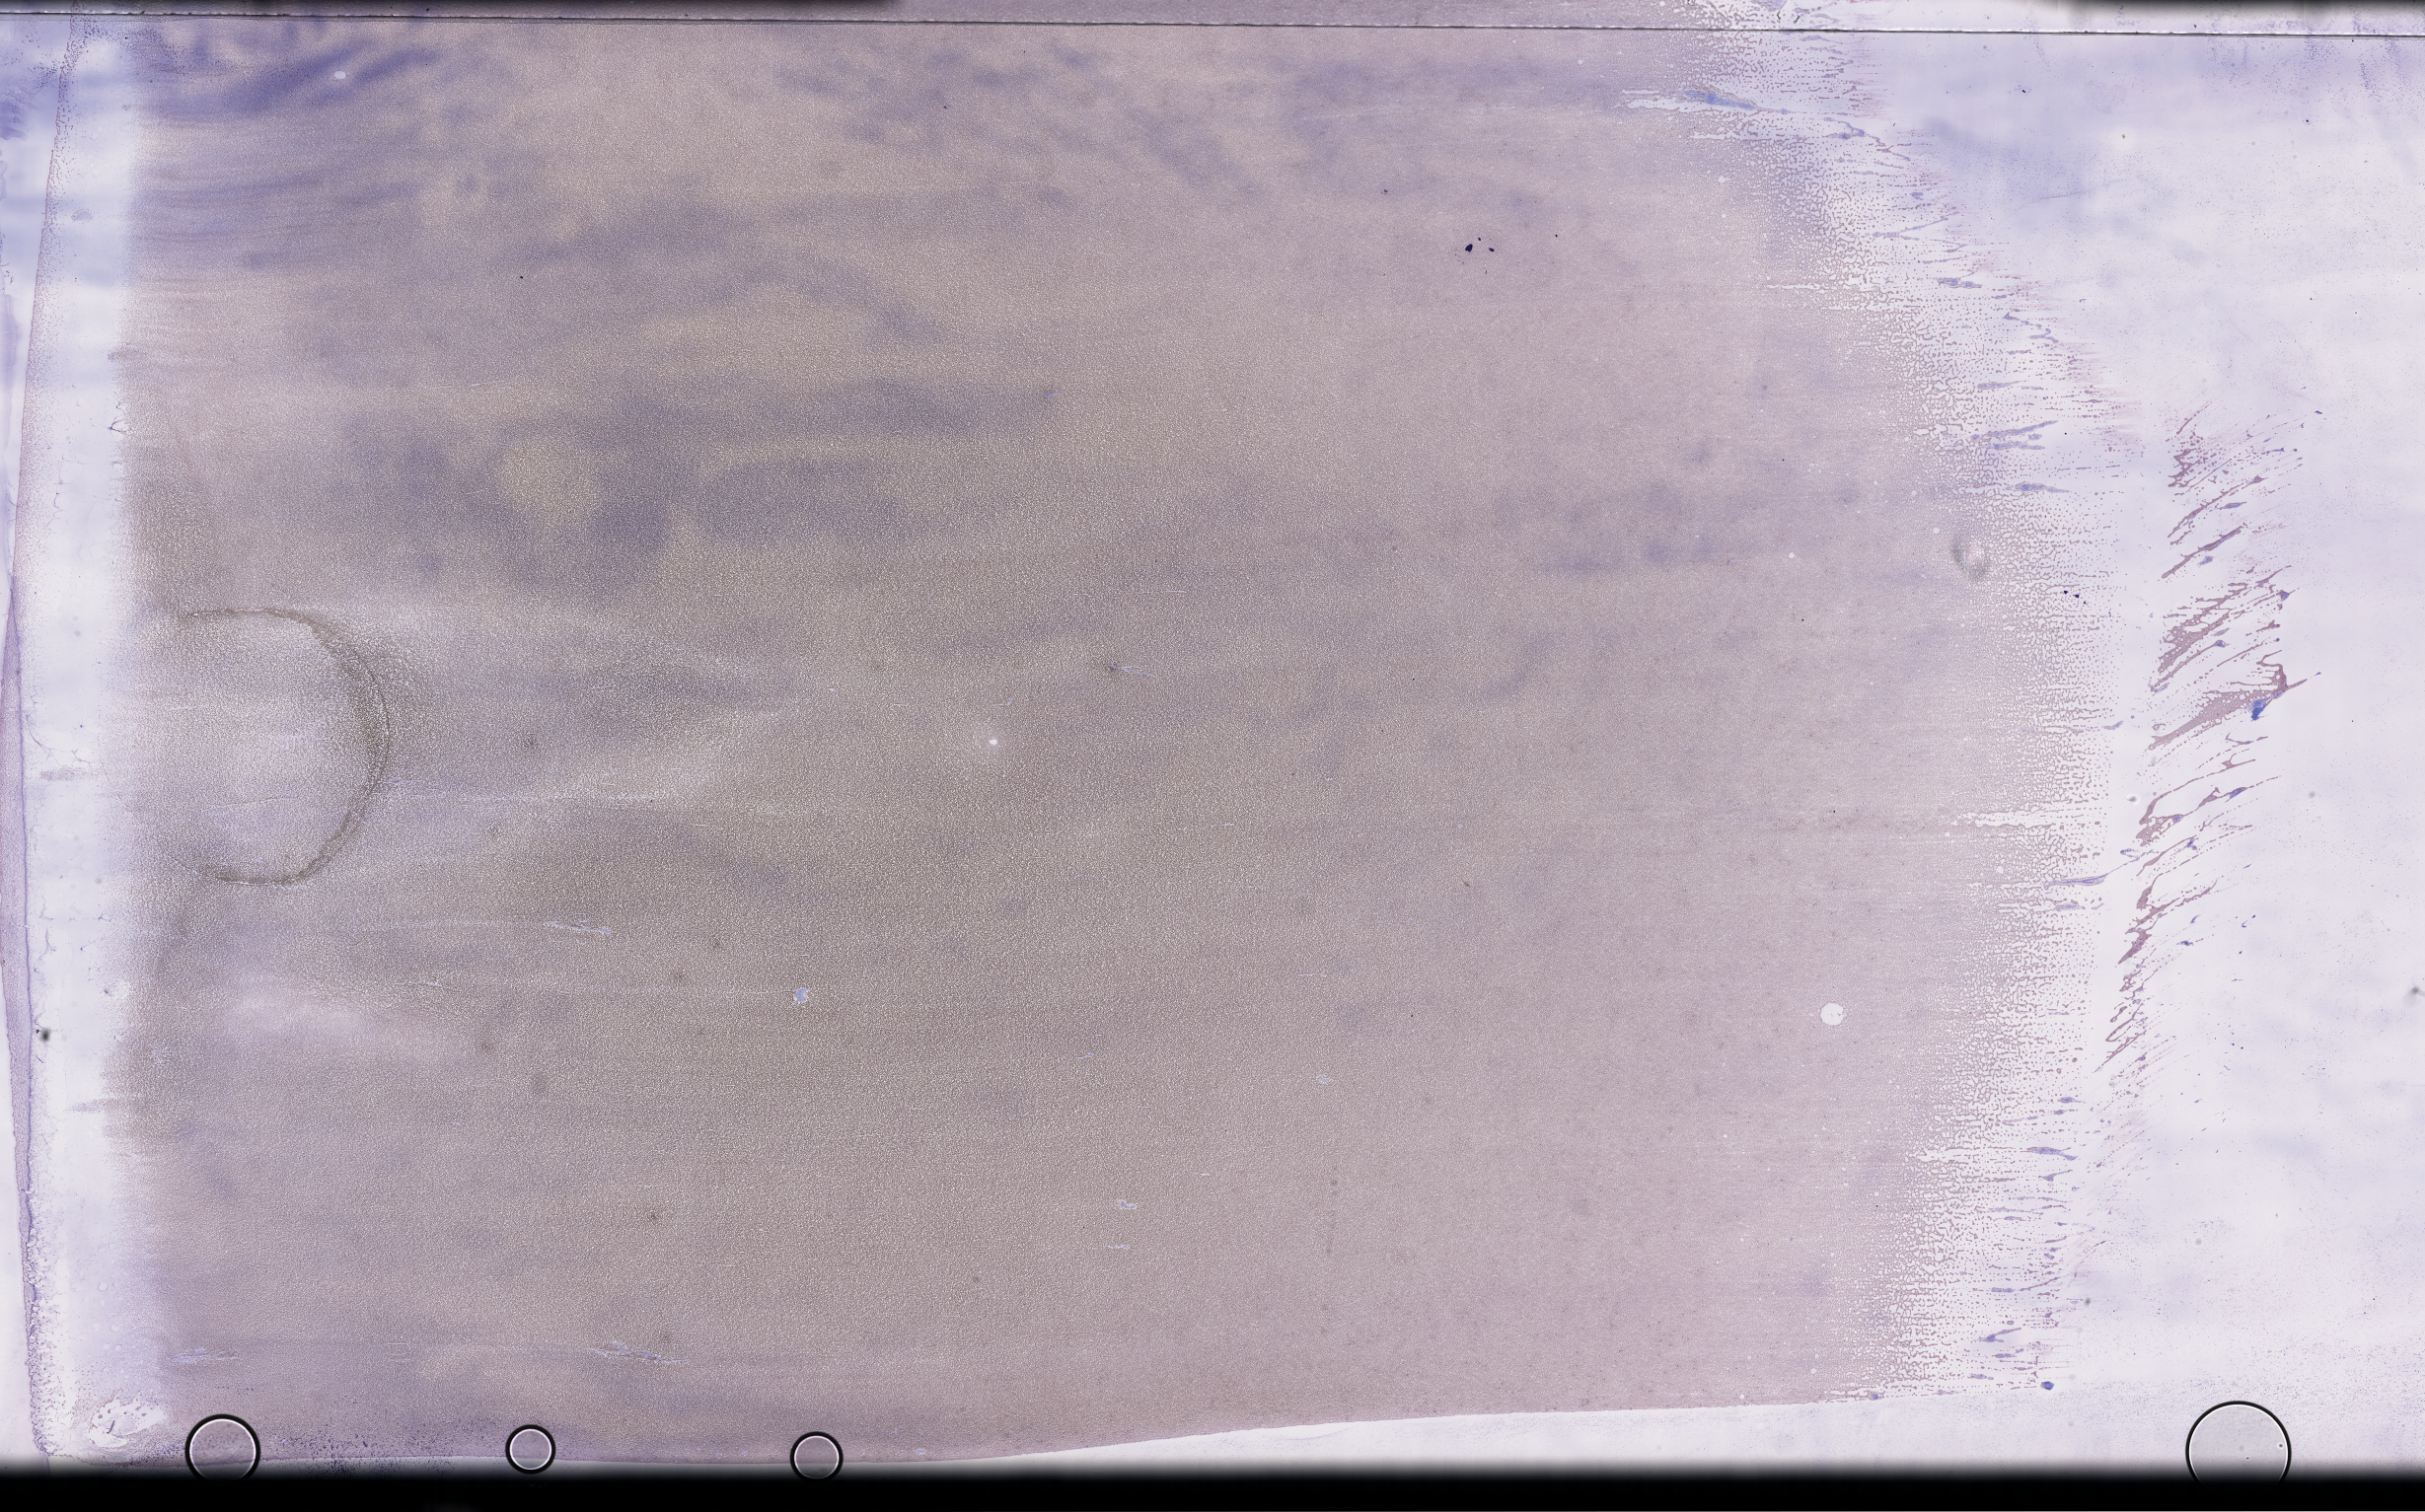
Wright-Giemsa-stained whole blood smear, whole-slide image — low-resolution overview of the scanned area, about 39.7 x 24.8 mm. EDTA-anticoagulated smear. Collected on treatment. Patient sex: male.
• from a patient with: Plasma Cell Myeloma